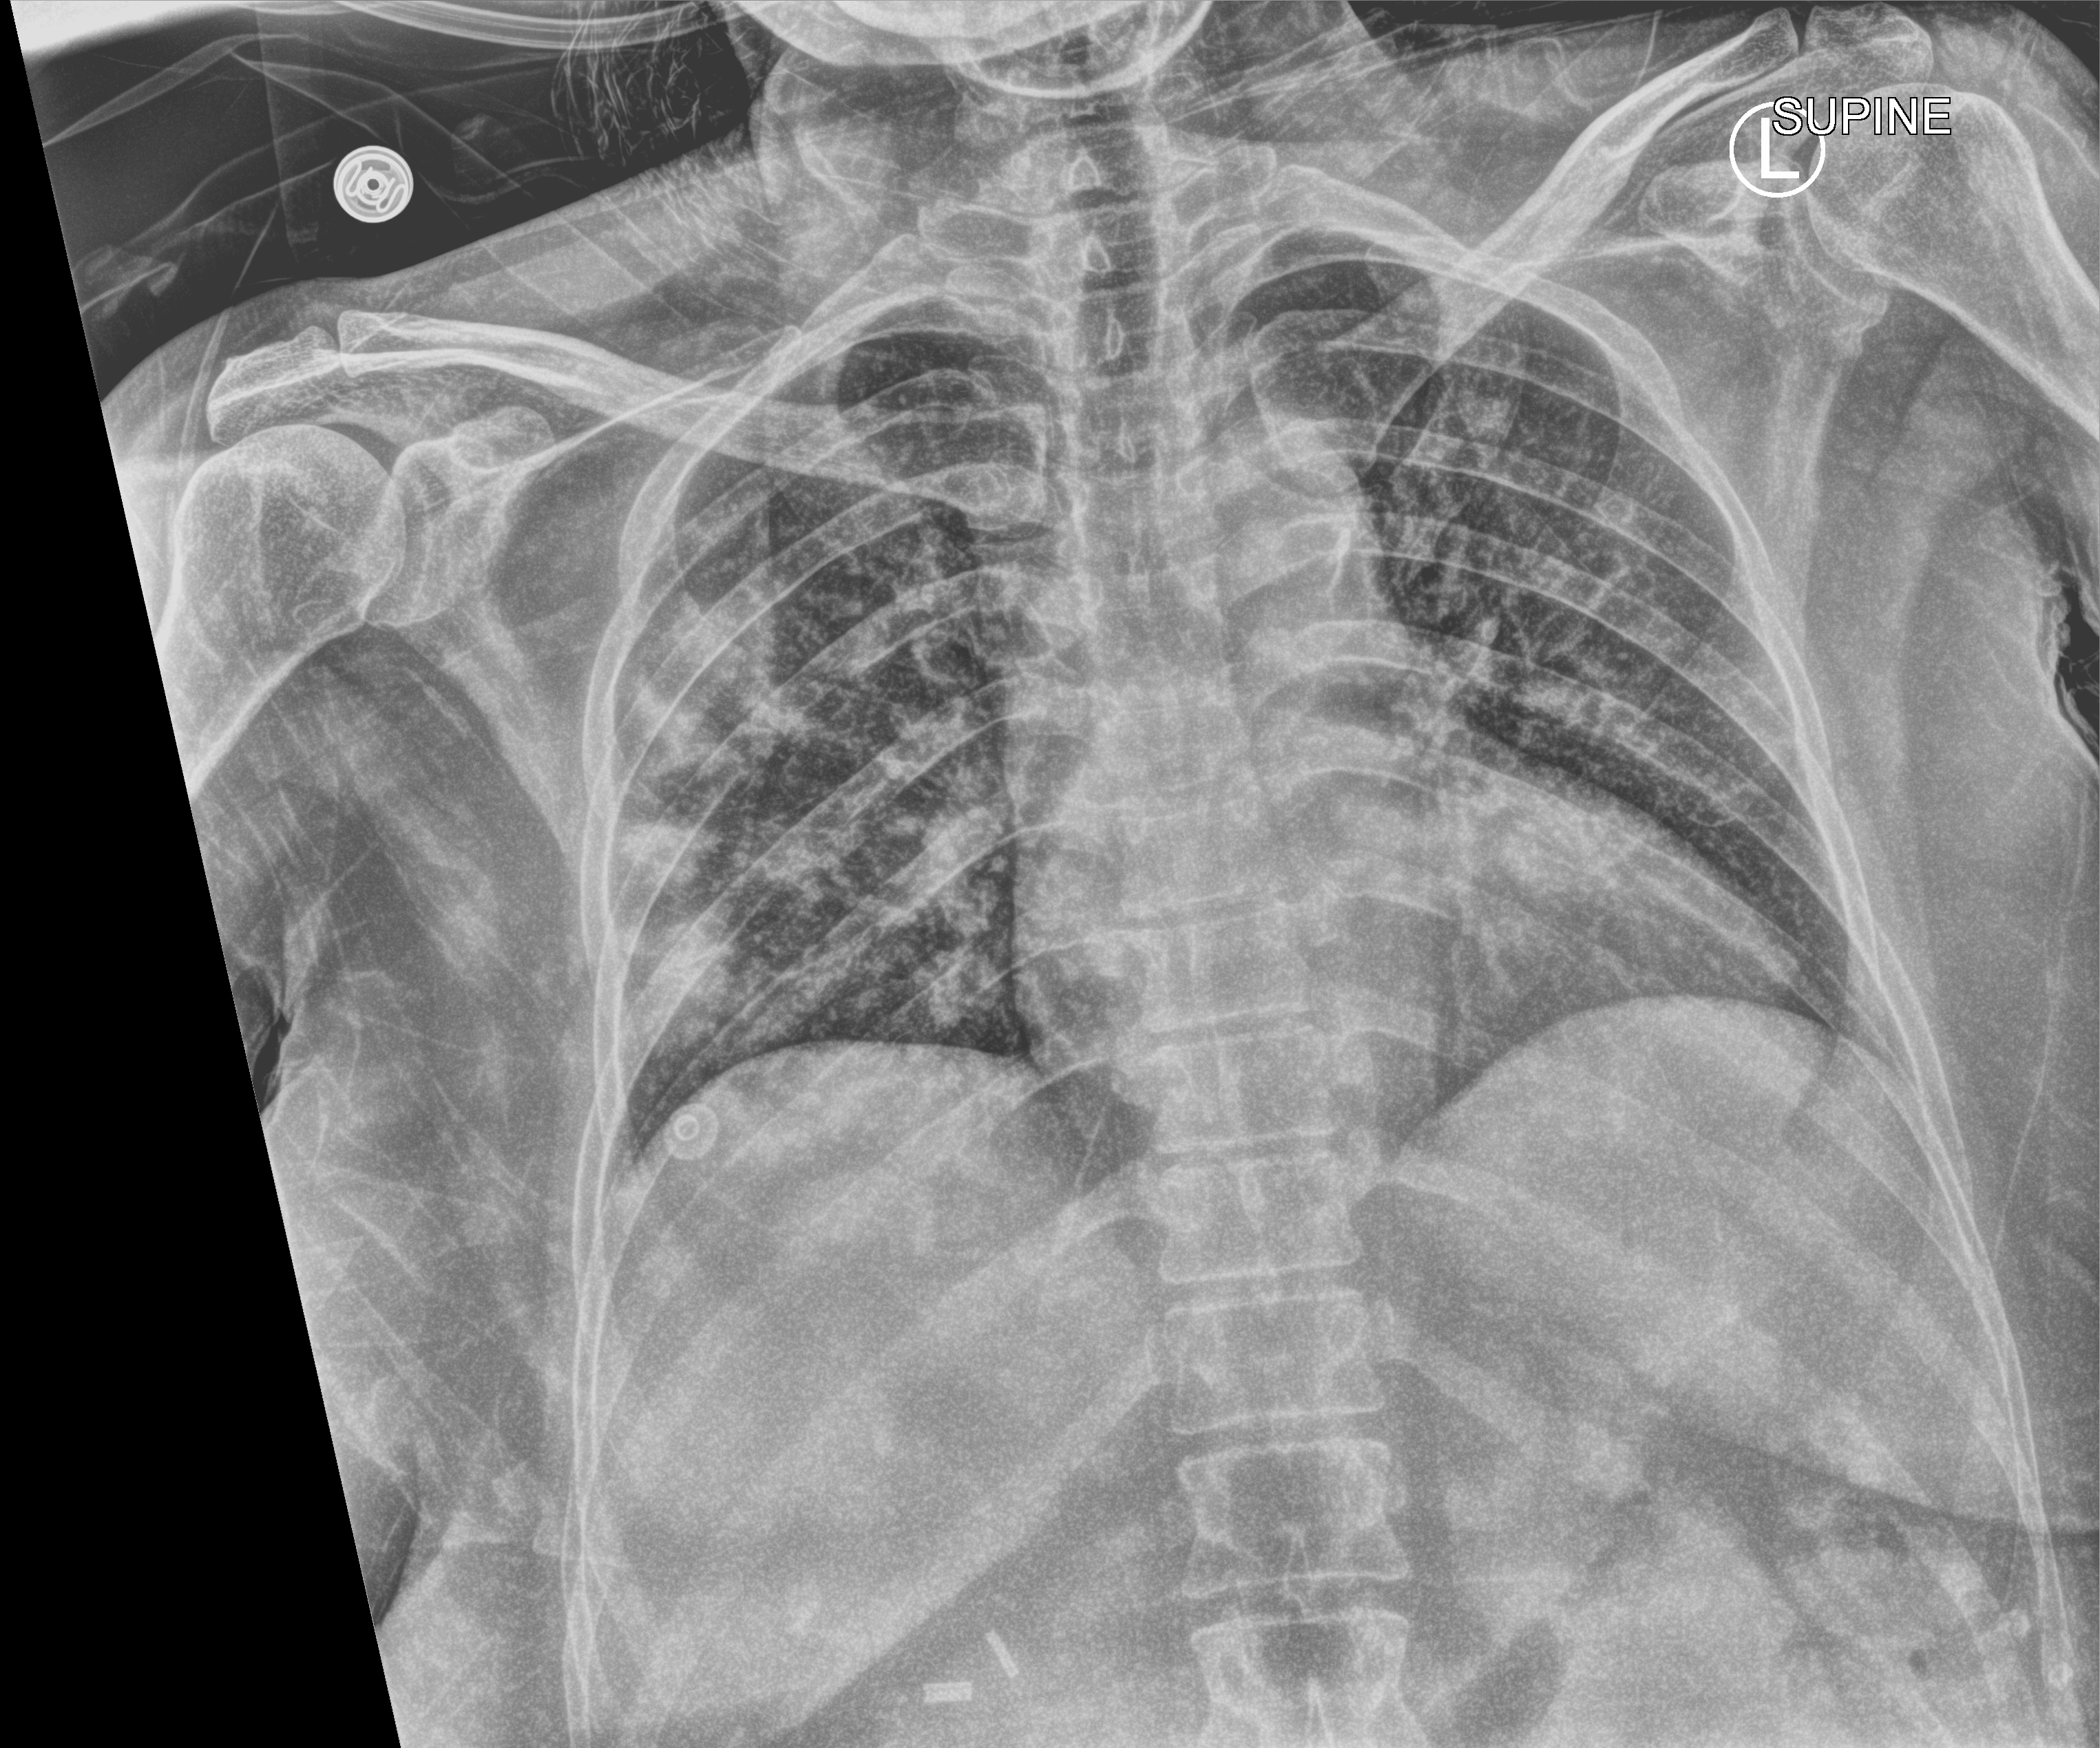
Bedside chest radiograph (computed radiography), anteroposterior (AP) projection. Female patient hospitalised with COVID-19, age 18–59 years.
Hospital-stay facts (about this admission, not read from this image; timing relative to this image not recorded):
- hypertension (admission record): yes
- diabetes (admission record): yes
- admitted to intensive care during this hospital stay: no